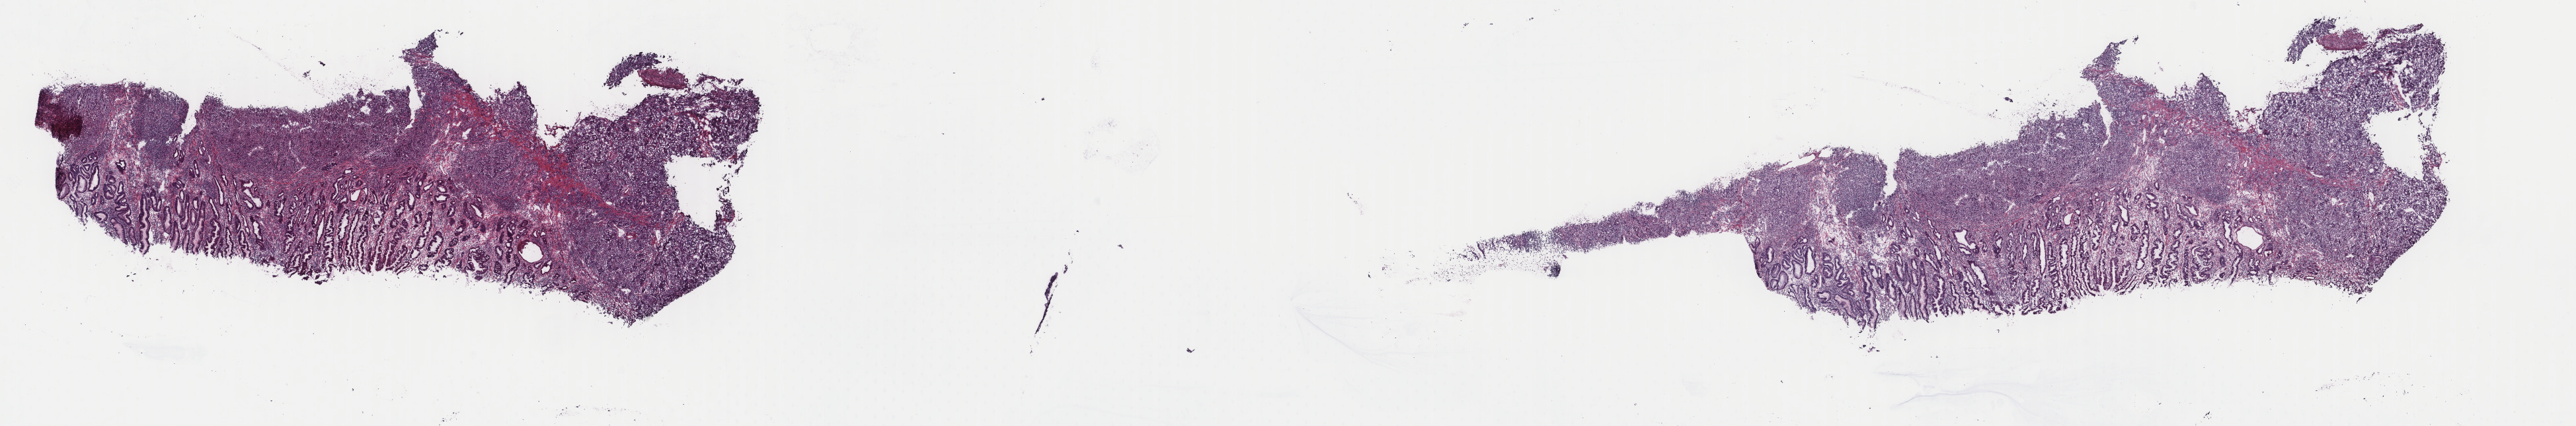
Whole-slide histology image, Hematoxylin and eosin (H&E) stained — a low-resolution overview of the entire scanned area, about 30.9 x 5.1 mm. Frozen section from the top of the tissue portion. Stomach, primary tumour sample. Female, age 53 years at initial diagnosis. Histologic grade: G3 (poorly differentiated). Slide review estimates, as recorded: tumour cells 60%, tumour nuclei 75%, normal cells 40%, stromal cells 0%, necrosis 0%. Infiltration values recorded for this section: lymphocyte infiltration 3%, monocyte infiltration 0%, neutrophil infiltration 0%.
* TNM: T2 N2 M0
* diagnosis: Tubular adenocarcinoma
* AJCC pathologic stage: IIB
* lymph nodes positive (case pathology): 4 of 21 examined